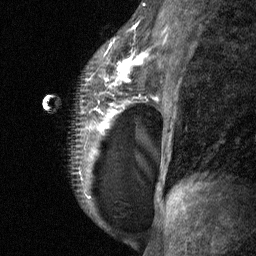
Breast MRI (dynamic contrast-enhanced), one sagittal slice. Position 44 of 64 along the scan axis. Dynamic contrast-enhanced study with each time point stored as its own series, time point 2 of 3 at this slice position (early post-contrast, ordered by acquisition time). 1.5 T. TE 4.8 ms, TR 27 ms. 2 mm slice thickness. 256 × 256 image matrix, field of view 180 × 180 mm. Female patient, age 34 years. From the clinical record (not read from this slice): setting: breast cancer imaged before/during neoadjuvant chemotherapy; receptor status: HR-positive, HER2-negative.
Outlined on this slice (semi-automatically segmented with operator editing):
- analysis volume of interest (the breast-tissue region the enhancement analysis was run in; not a lesion): box from (x=42, y=23) to (x=157, y=197) px
- tumour enhancement mask (voxels above the 90 % enhancement threshold inside the analysis volume of interest): (x=86, y=43)–(x=146, y=132)